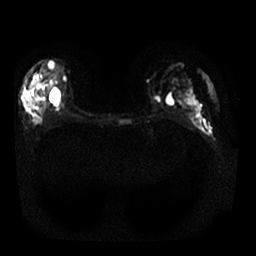
Breast MRI, one axial slice. Slice 14 of 30 in the series (ordered by position). Diffusion-weighted series; image 2 of 4 stored at this slice position (different b-values; order by instance number). 1.5 T. 256 × 256 image matrix, field of view 340 × 340 mm. Female patient.
Annotated regions visible in this slice (outlined manually by an expert reader):
- tumour on diffusion-weighted imaging: bounding box [x1, y1, x2, y2] px = [25, 98, 50, 117]